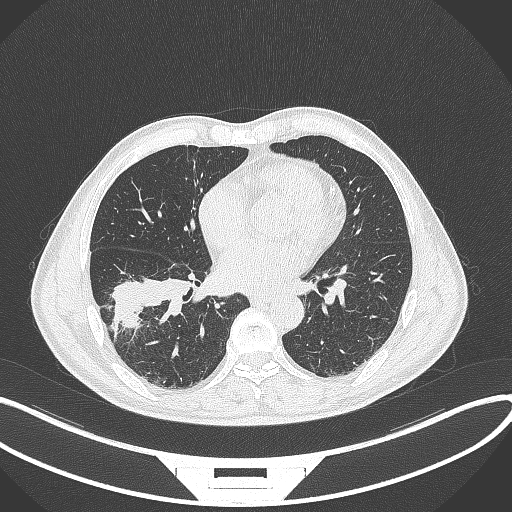
Chest CT, one axial slice; slice 158 of 364 in the series (ordered by position); reconstruction kernel B70f; 120 kVp; lung window (W 1500 / L -600 HU); 1 mm slice thickness; 512 × 512 image matrix, field of view 400 × 400 mm. Patient: male, 58 years. Case-level facts recorded for this patient, not image findings: clinical TNM (as recorded): T3 N0 M0.
Outlined on this slice (rectangle marked by the reading radiologist):
- lung tumour (recorded histology: squamous cell carcinoma): bounding box (x1, y1, x2, y2) in pixels: (104, 270, 190, 331)